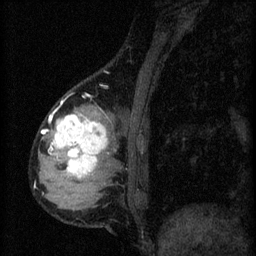
Breast MRI (dynamic contrast-enhanced), one sagittal slice. Slice 16 of 60 in the series (ordered by position). 3 images stored at this slice position (order not interpretable as contrast timing). 1.5 T. TE 4.2 ms, TR 8.2 ms. 256 × 256 image matrix. Female patient, age 37 years.
Annotated regions visible in this slice (semi-automatically segmented with operator editing):
- analysis volume of interest (the breast-tissue region the enhancement analysis was run in; not a lesion): bounding box (x1, y1, x2, y2) in pixels: (44, 100, 119, 197)
- tumour enhancement mask (voxels above the 70 % enhancement threshold inside the analysis volume of interest): (51, 114, 109, 179)